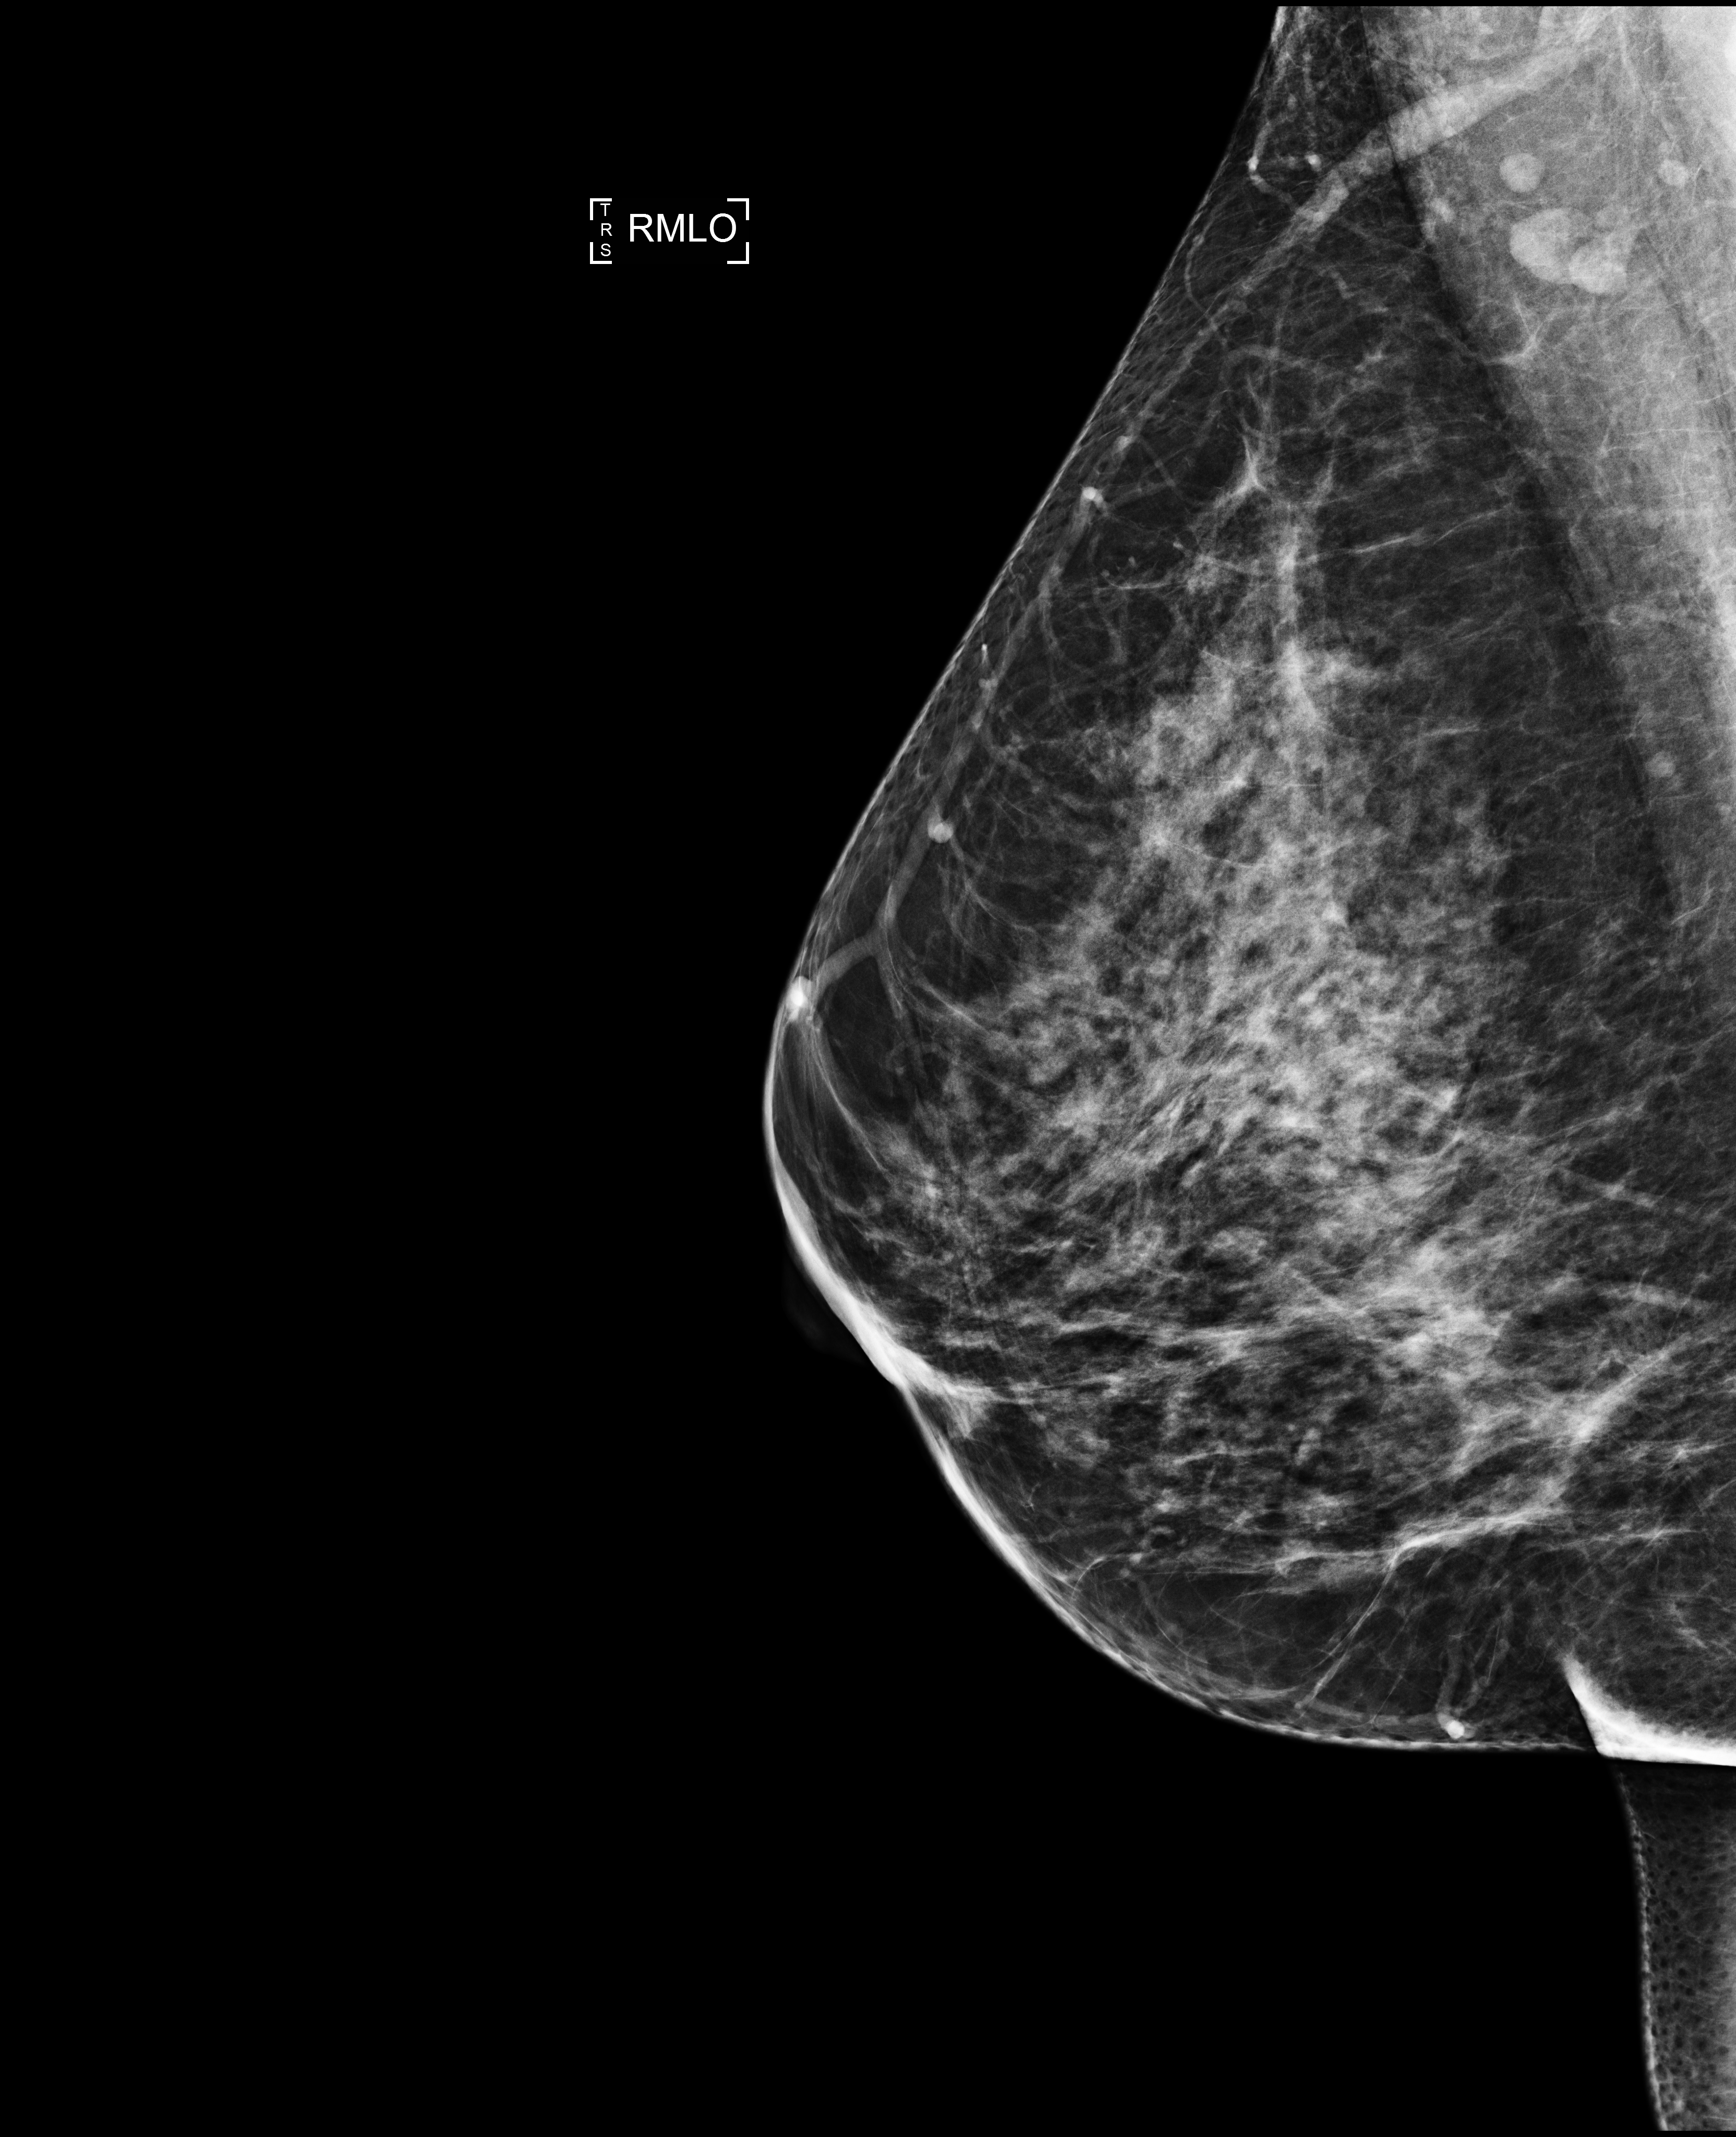
Full-field digital mammogram (FFDM), right breast, mediolateral oblique (MLO) view, annual screening mammography examination. Patient aged 44 years (female).
BI-RADS breast density category at the screening exam (both breasts, scale 1–4): 3. Final BI-RADS category for the screening round (tomosynthesis exam, both breasts): category 2. Recall: no recall after this screen.